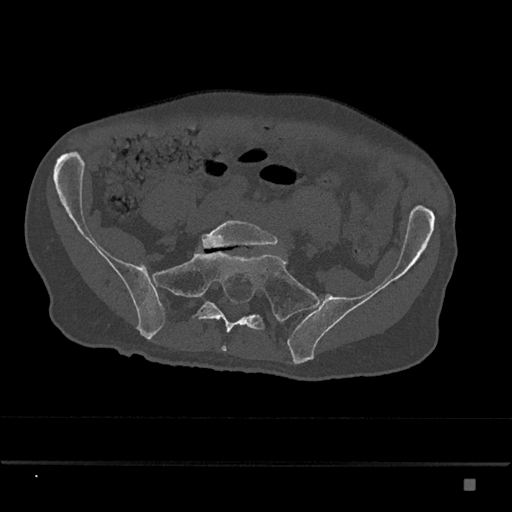
CT including the spine, one axial slice. Slice 225 of 797 in the series (ordered by position). Bone window (W 1800 / L 400 HU). 512 × 512 image matrix. Male patient, age 72 years. From the clinical record (not read from this slice): primary cancer: prostate.
Outlined on this slice (semi-automatically segmented with operator editing):
- L5 vertebra: bounding box (x1, y1, x2, y2) in pixels: (201, 220, 279, 249)